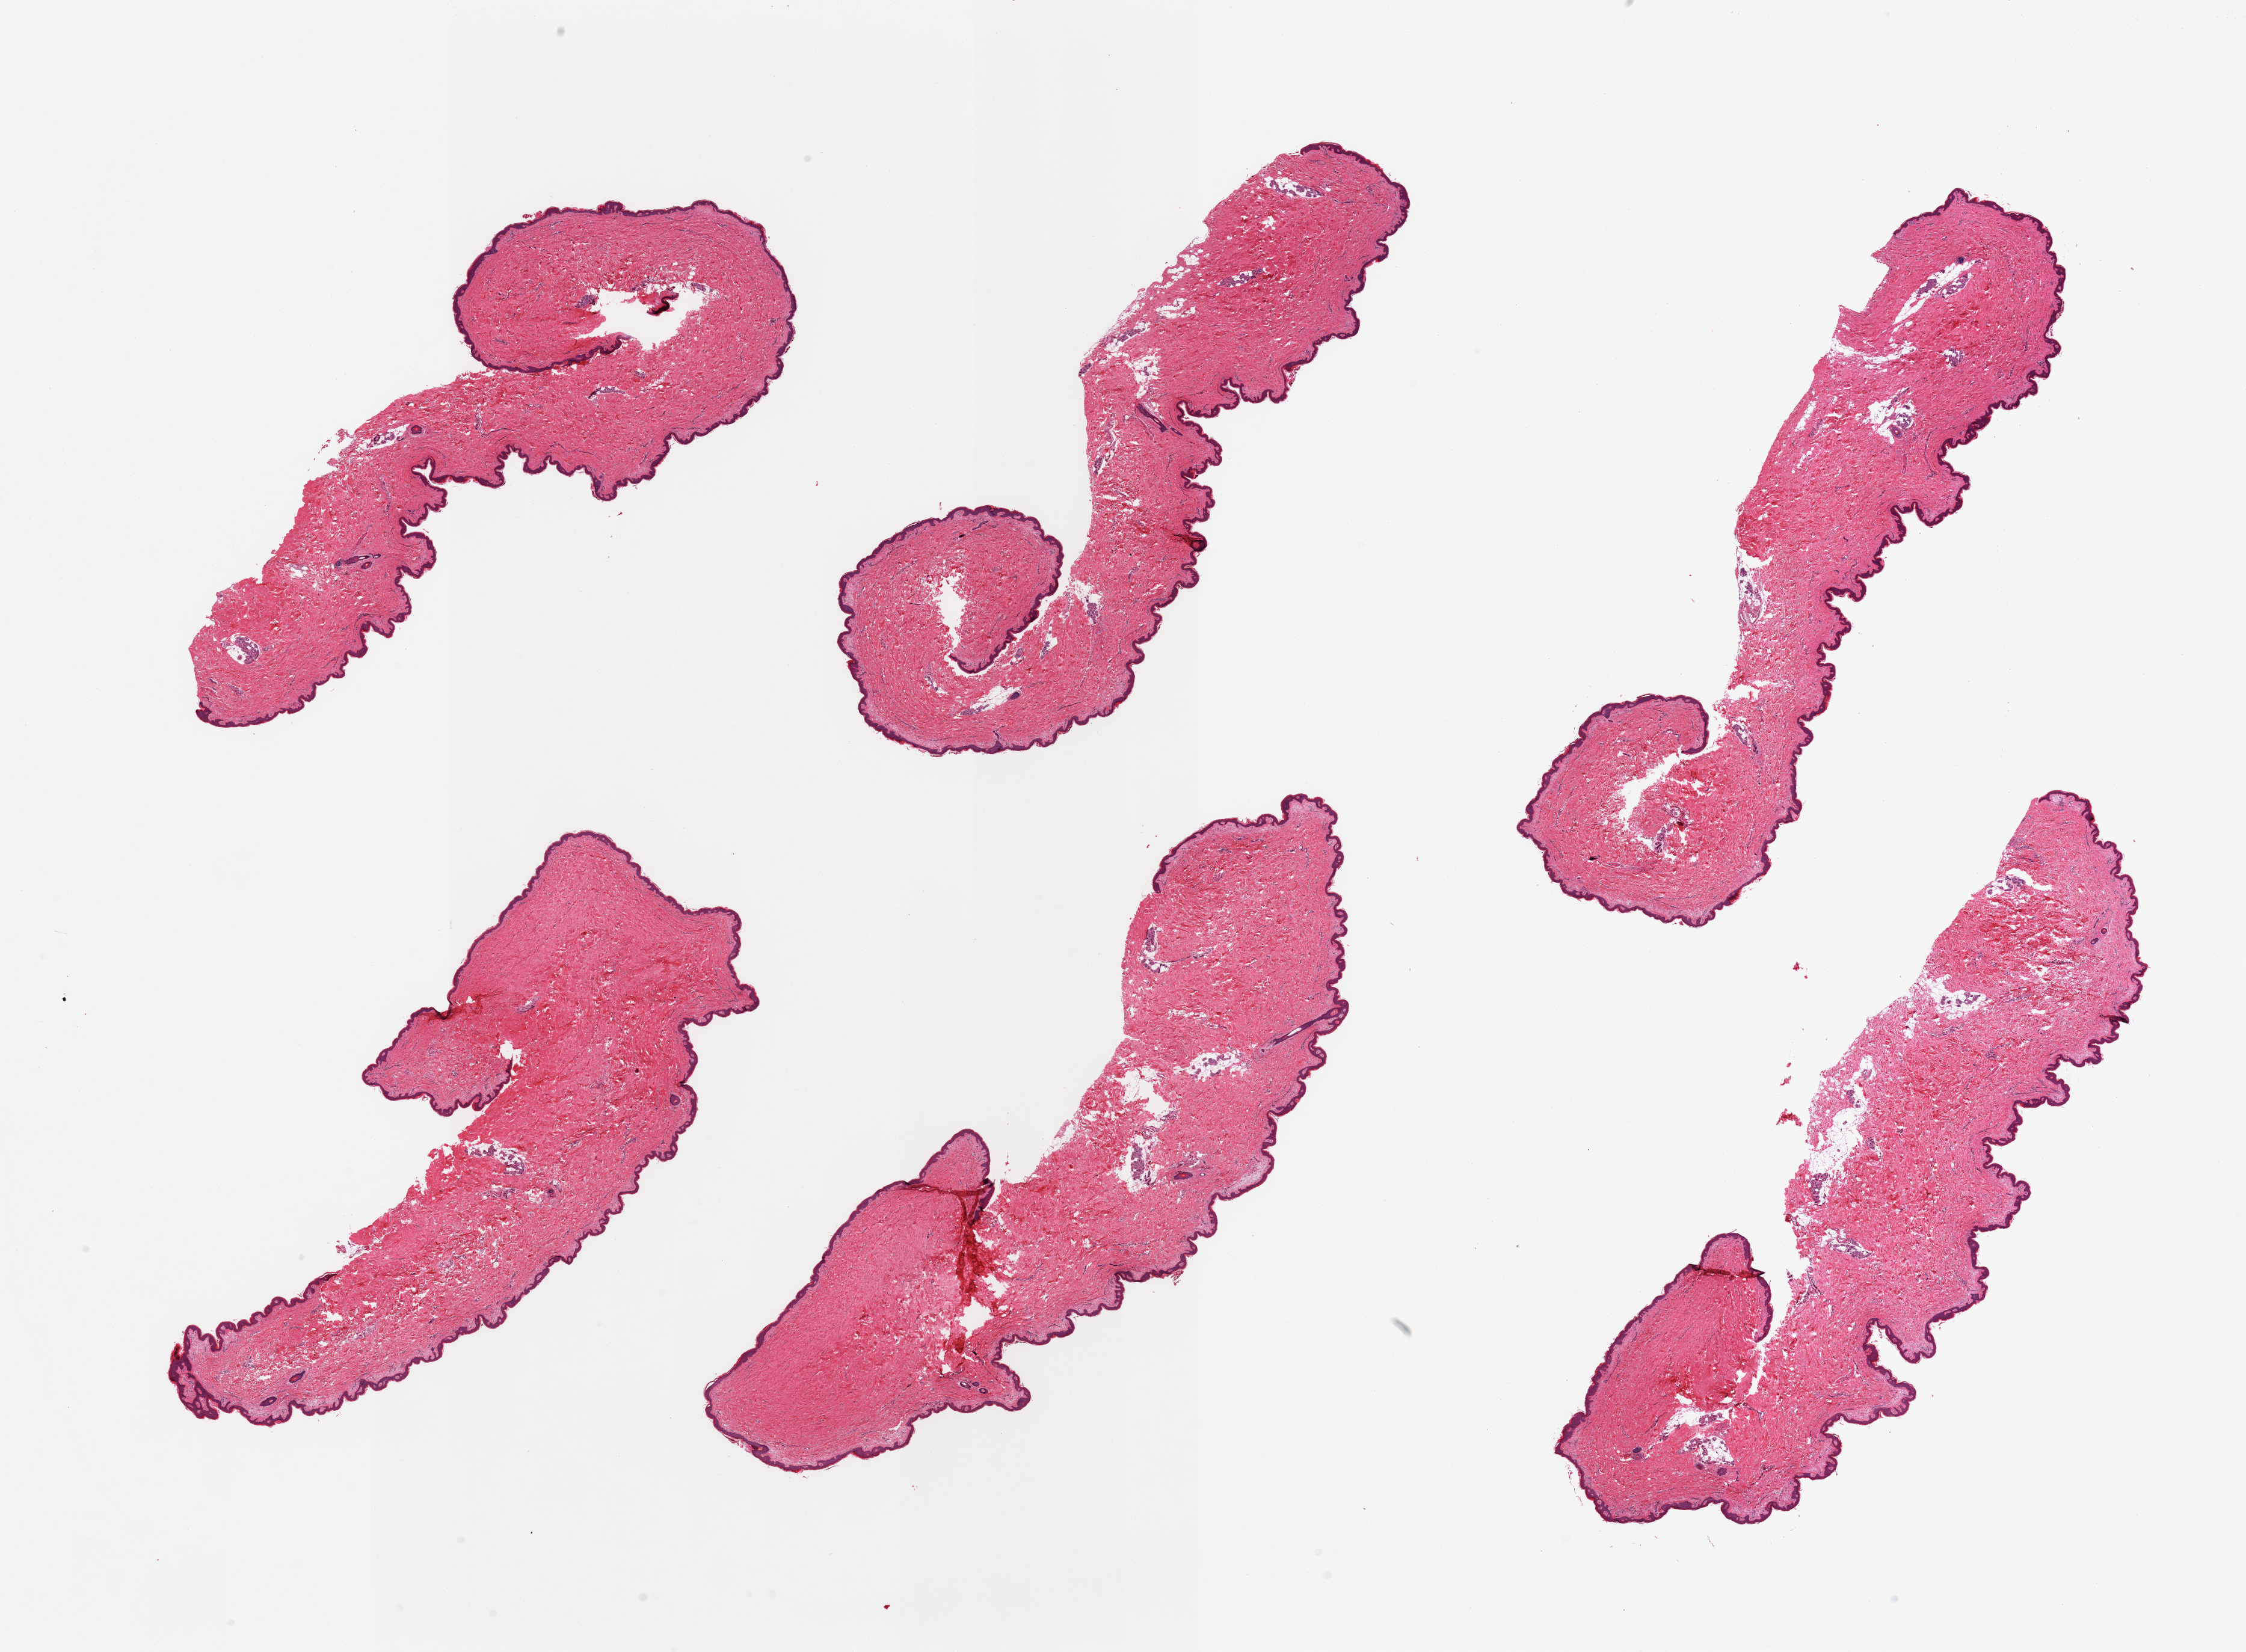
Digitized hematoxylin and eosin (H&E)-stained section — a low-resolution overview of the entire scanned area, about 29.5 x 21.7 mm, PAXgene-fixed, paraffin-embedded tissue, target tissue: skin of suprapubic region, donor tissue sample. Donor sex: female.
Review note (as recorded): 6 pieces, minimal dermal fat; squamous epithelium is ~40 microns.